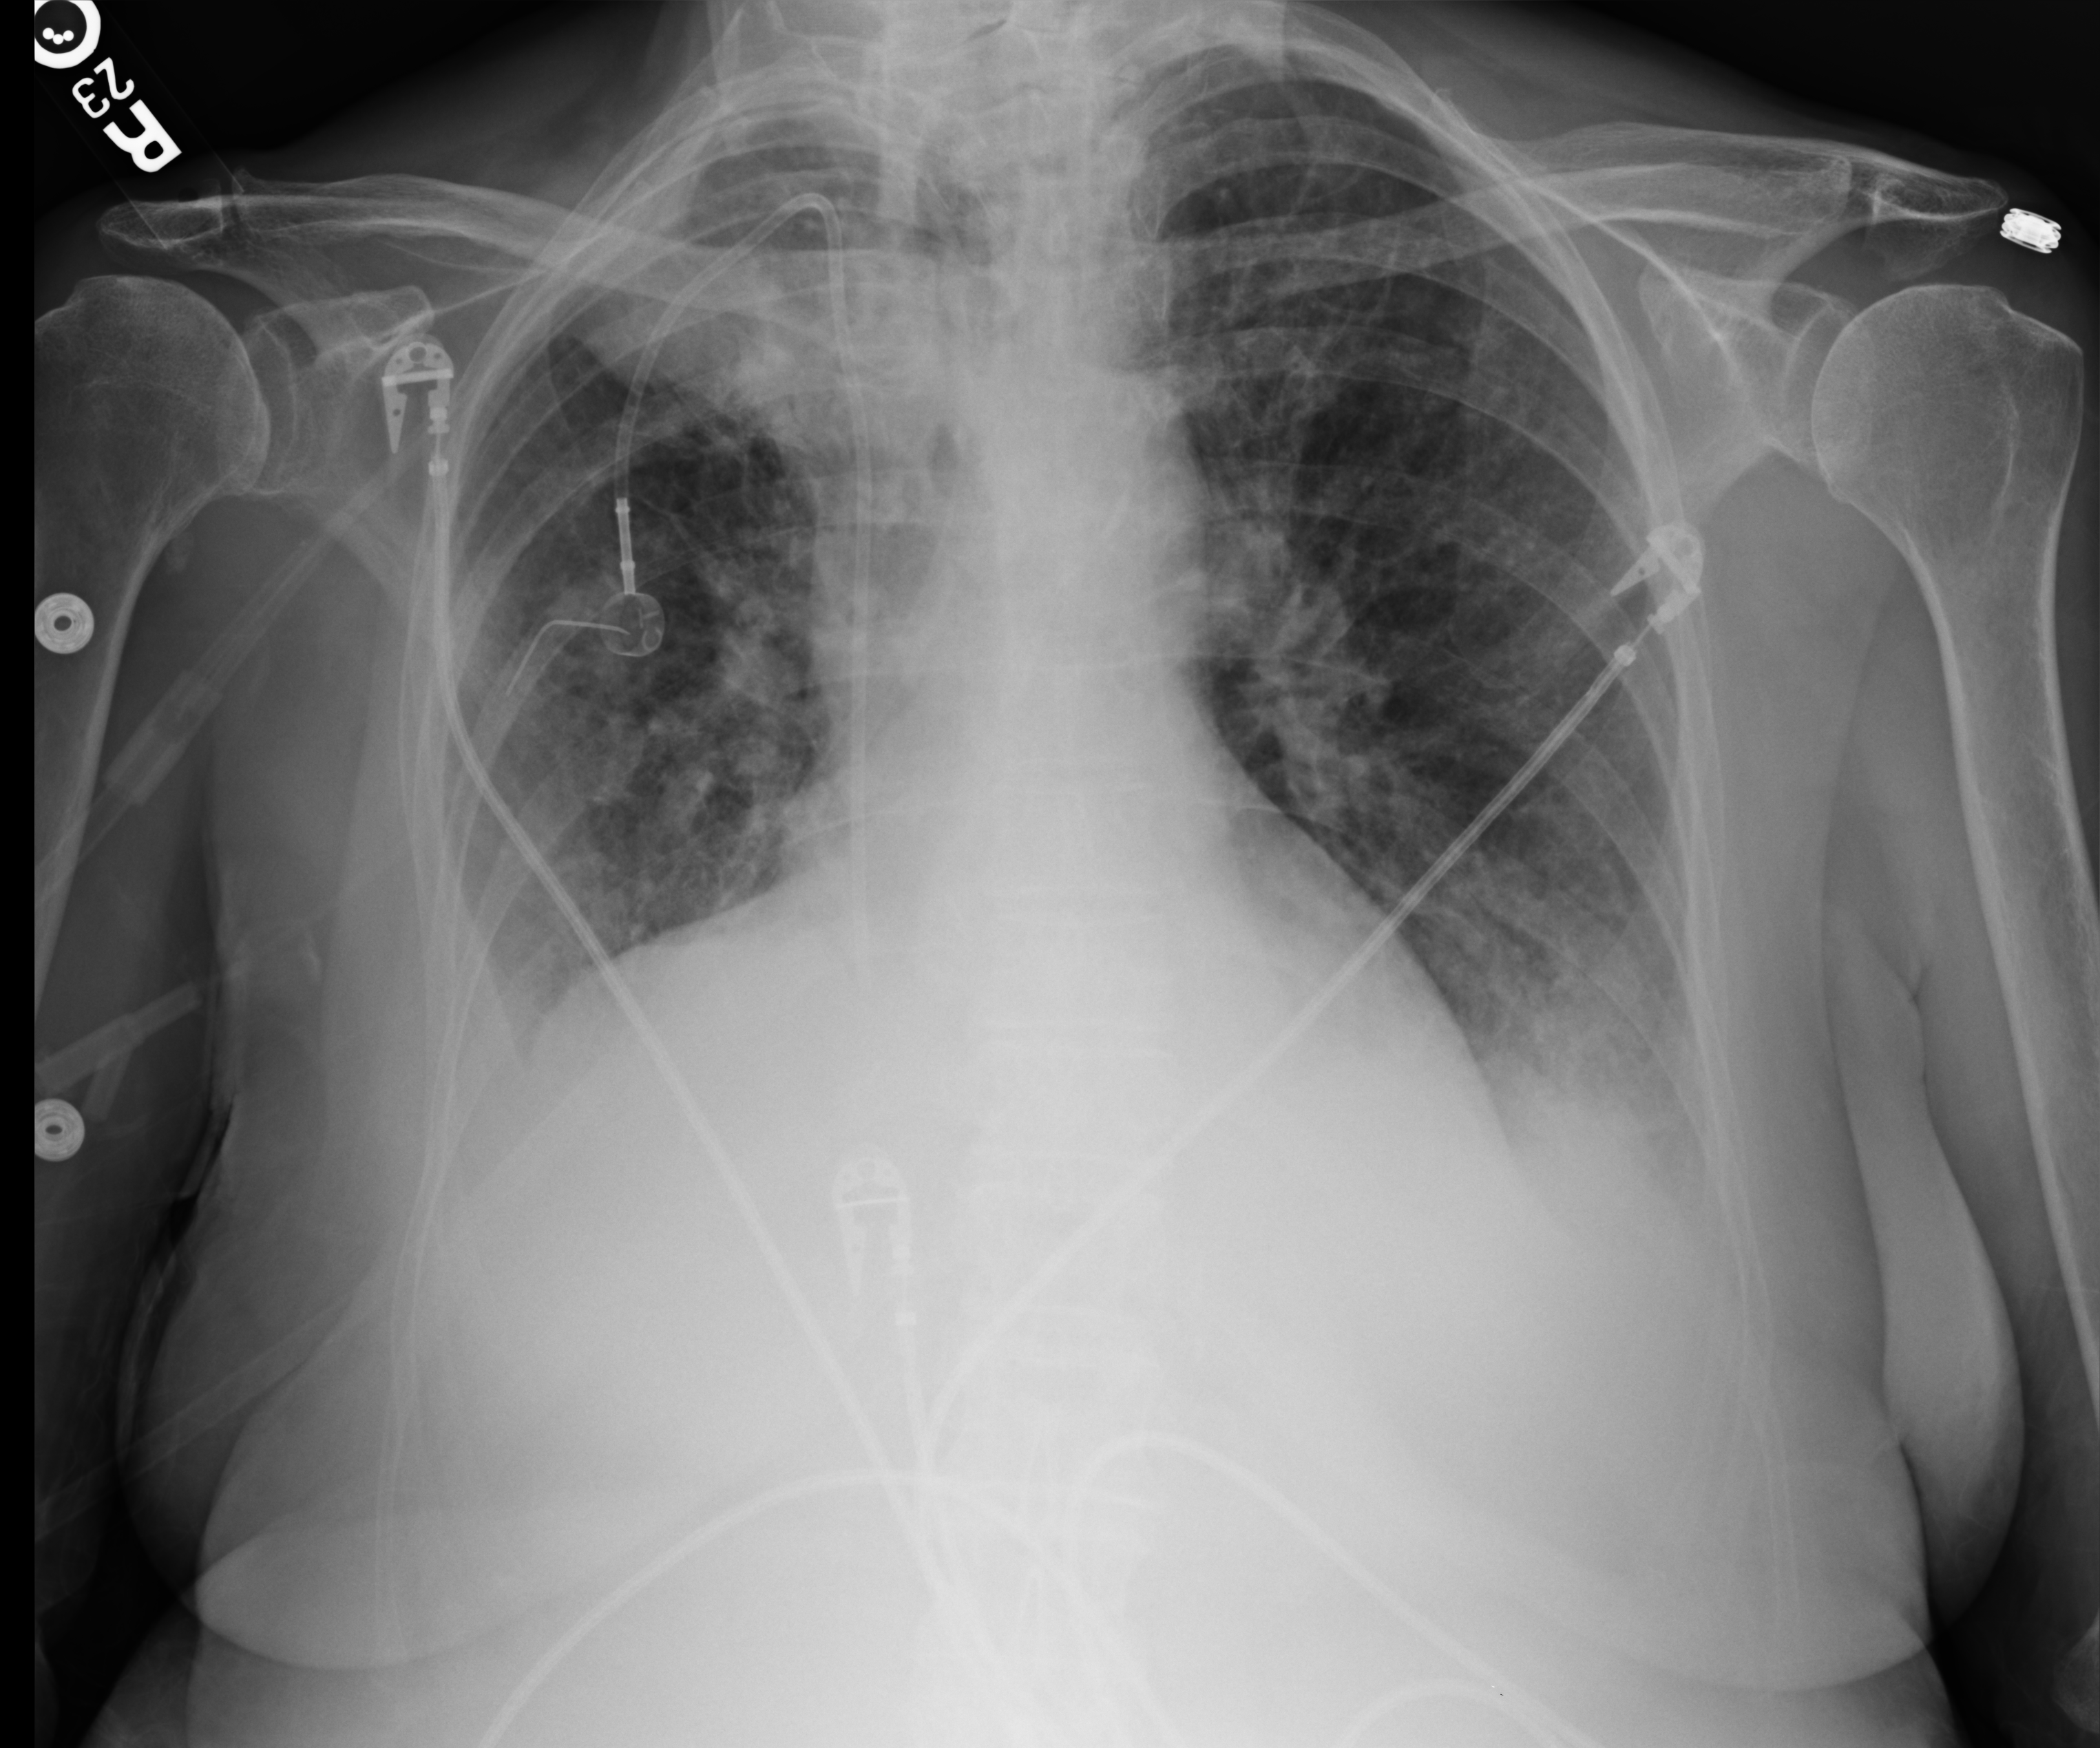
Chest X-ray (portable), anteroposterior (AP) projection. Female patient hospitalised with COVID-19, age 60–74 years.
From the hospital-stay record, not from the radiograph (when in the stay this image was taken is not recorded): mechanically ventilated during this hospital stay: no; length of hospital stay: 8 days; admitted to intensive care during this hospital stay: no.